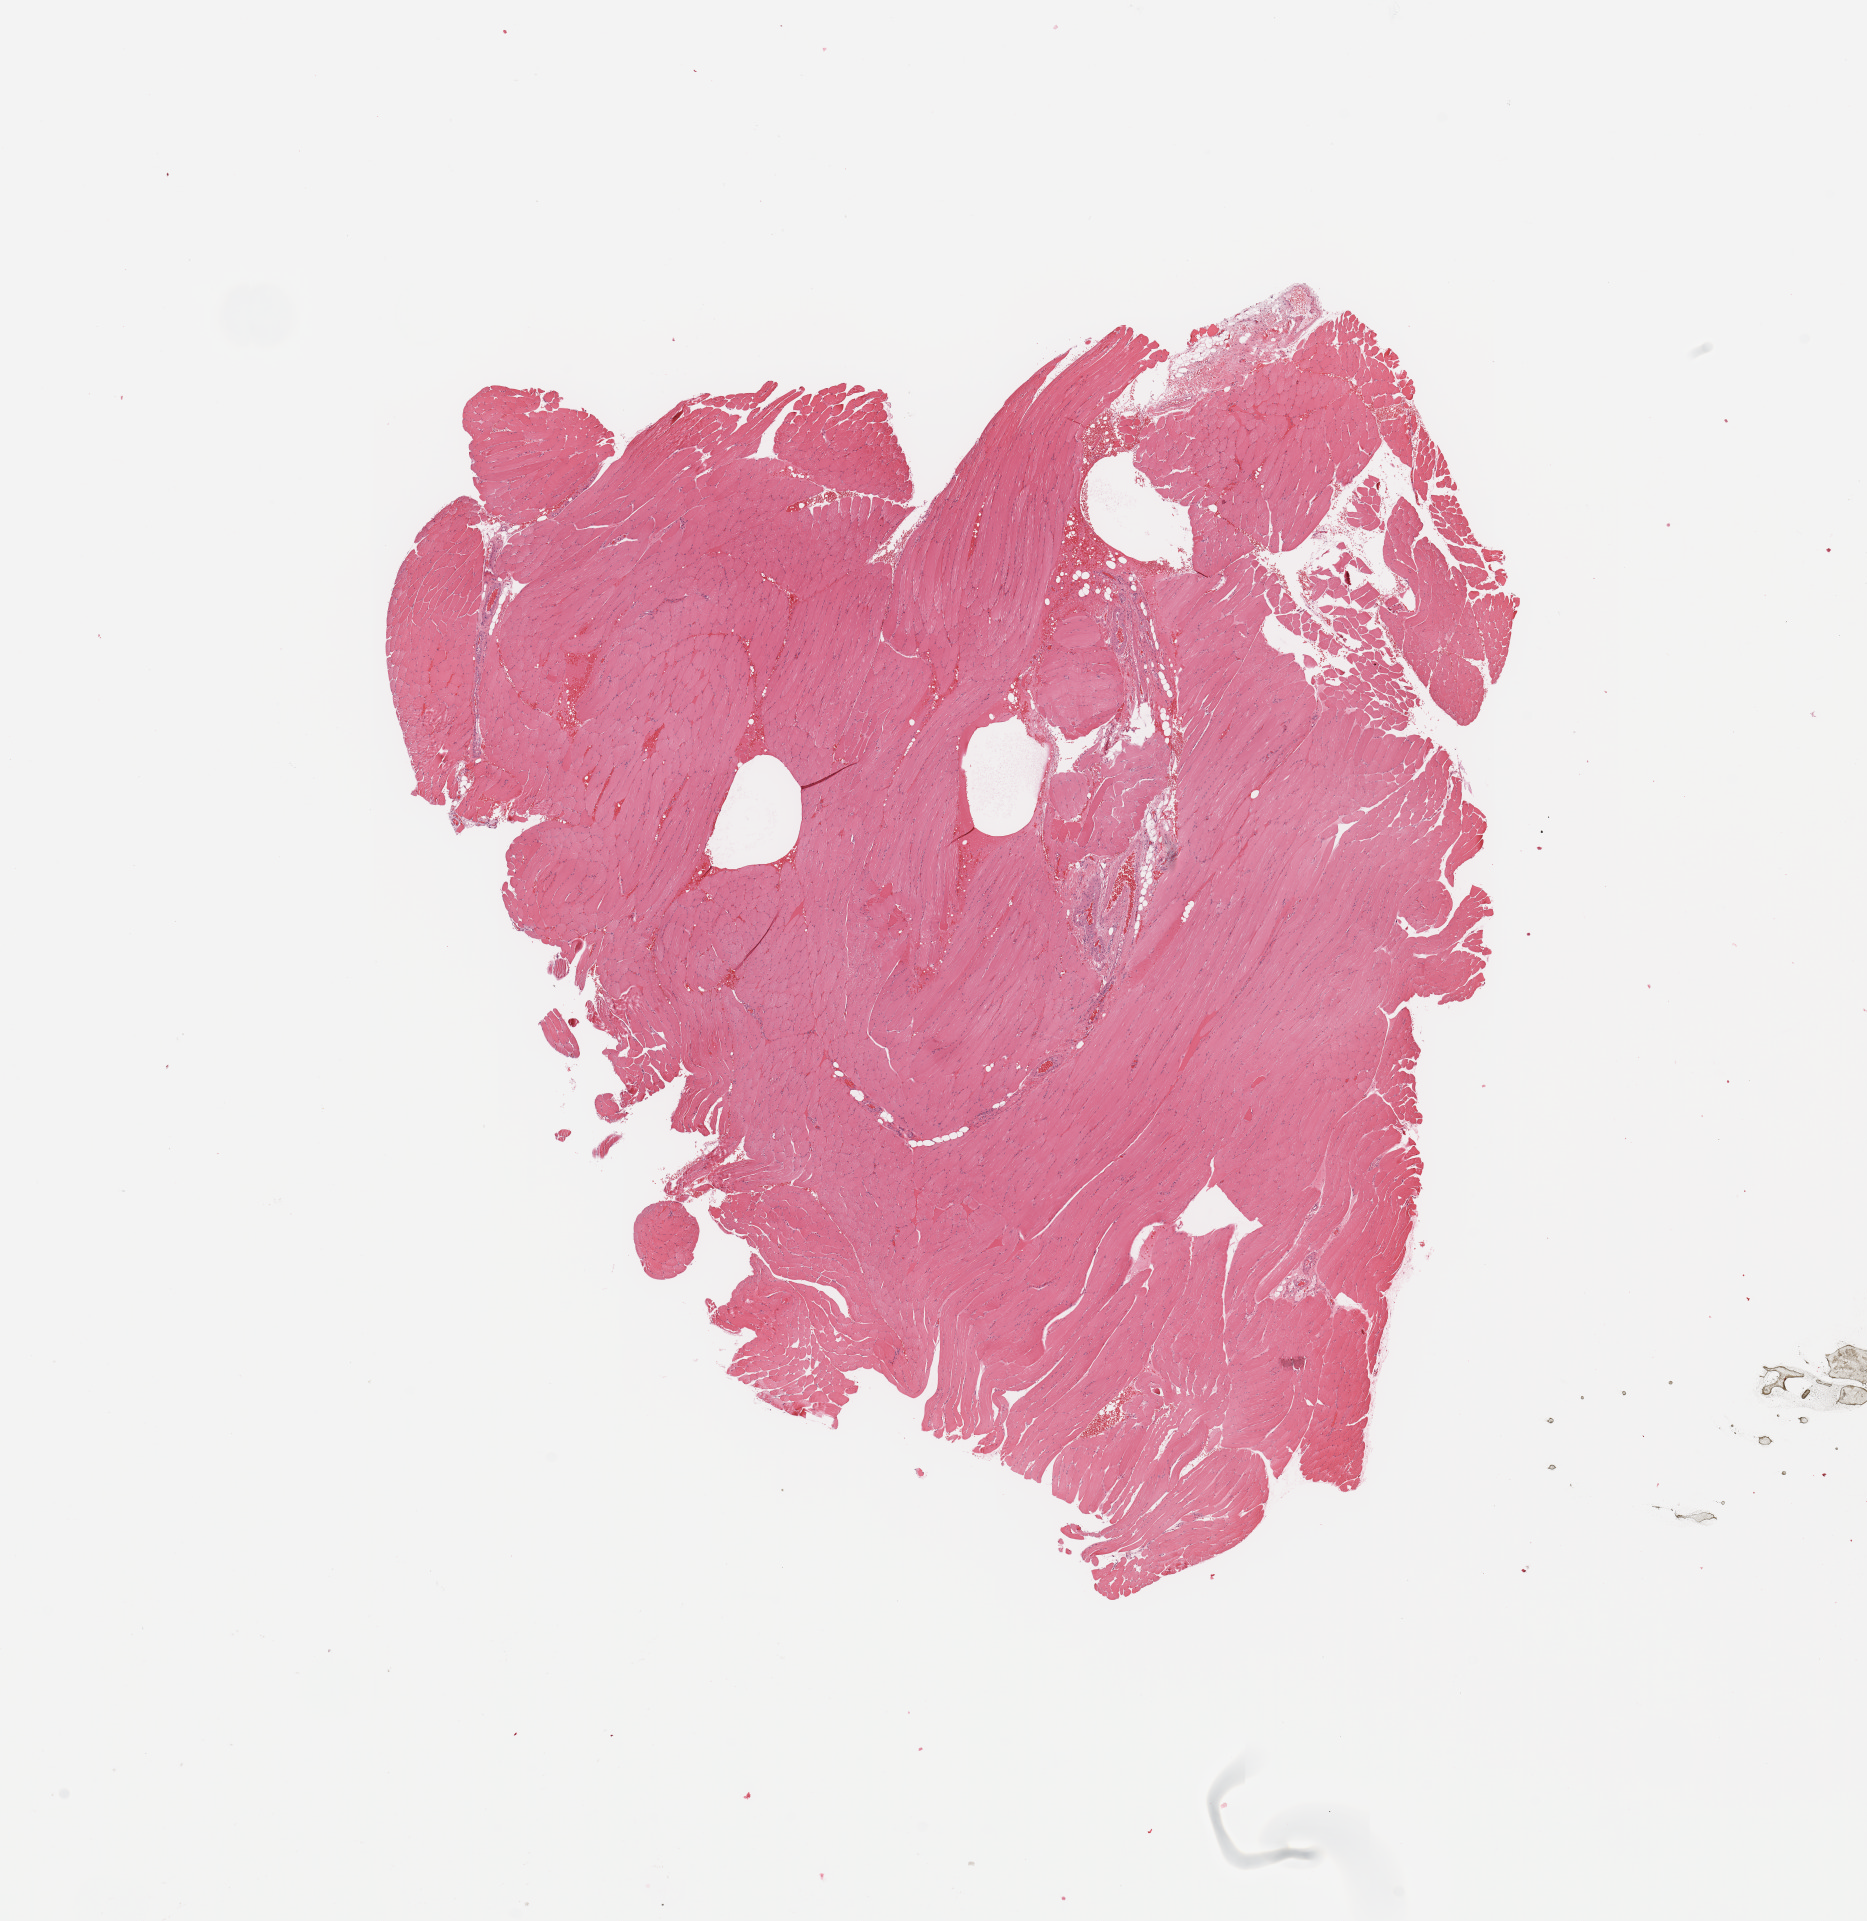
Digitized H&E tissue section (whole slide) — a low-resolution overview of the entire scanned area, about 14.8 x 15.2 mm. Normal (non-tumour) tissue sample. Patient: male, age 64 years.
This section: normal (non-tumour) tissue from the same patient. Patient diagnosis (cohort enrolment): sarcoma (site not recorded at cohort level).